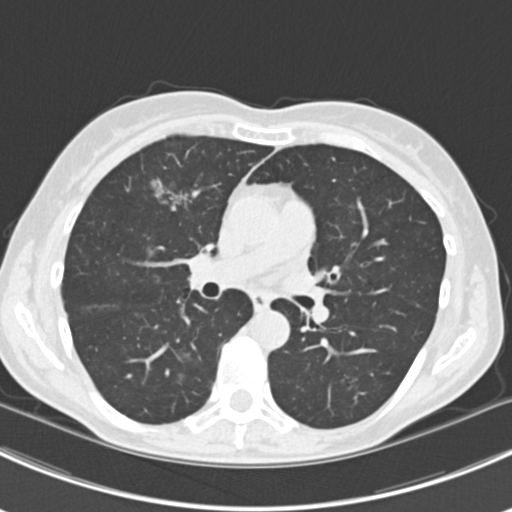
Chest CT (low-dose screening protocol), one axial image, first (baseline) screen, lung window (W 1500 / L -600 HU), 2 mm slice thickness, slice 82 of 224 in the series, 512 × 512 image matrix. Female participant, aged 63 years at enrolment. Current smoker at enrolment.
Expert reader's lesion annotation, bounding box [x1, y1, x2, y2] px = [144, 168, 202, 223]. The screening reader recorded 10 non-calcified nodules or masses ≥4 mm on this exam (right lower lobe, right lower lobe, left lower lobe, left lower lobe, right middle lobe, right lower lobe, left lower lobe, left upper lobe, right upper lobe, left upper lobe); which of them this box marks is not recorded. Later outcome: lung cancer diagnosed 751 days after this screen (after the third annual screen) — bronchiolo-alveolar adenocarcinoma, NOS, right upper lobe, right middle lobe, right lower lobe, left upper lobe, left lower lobe, moderately differentiated (G2), stage IV (AJCC 6th edition).